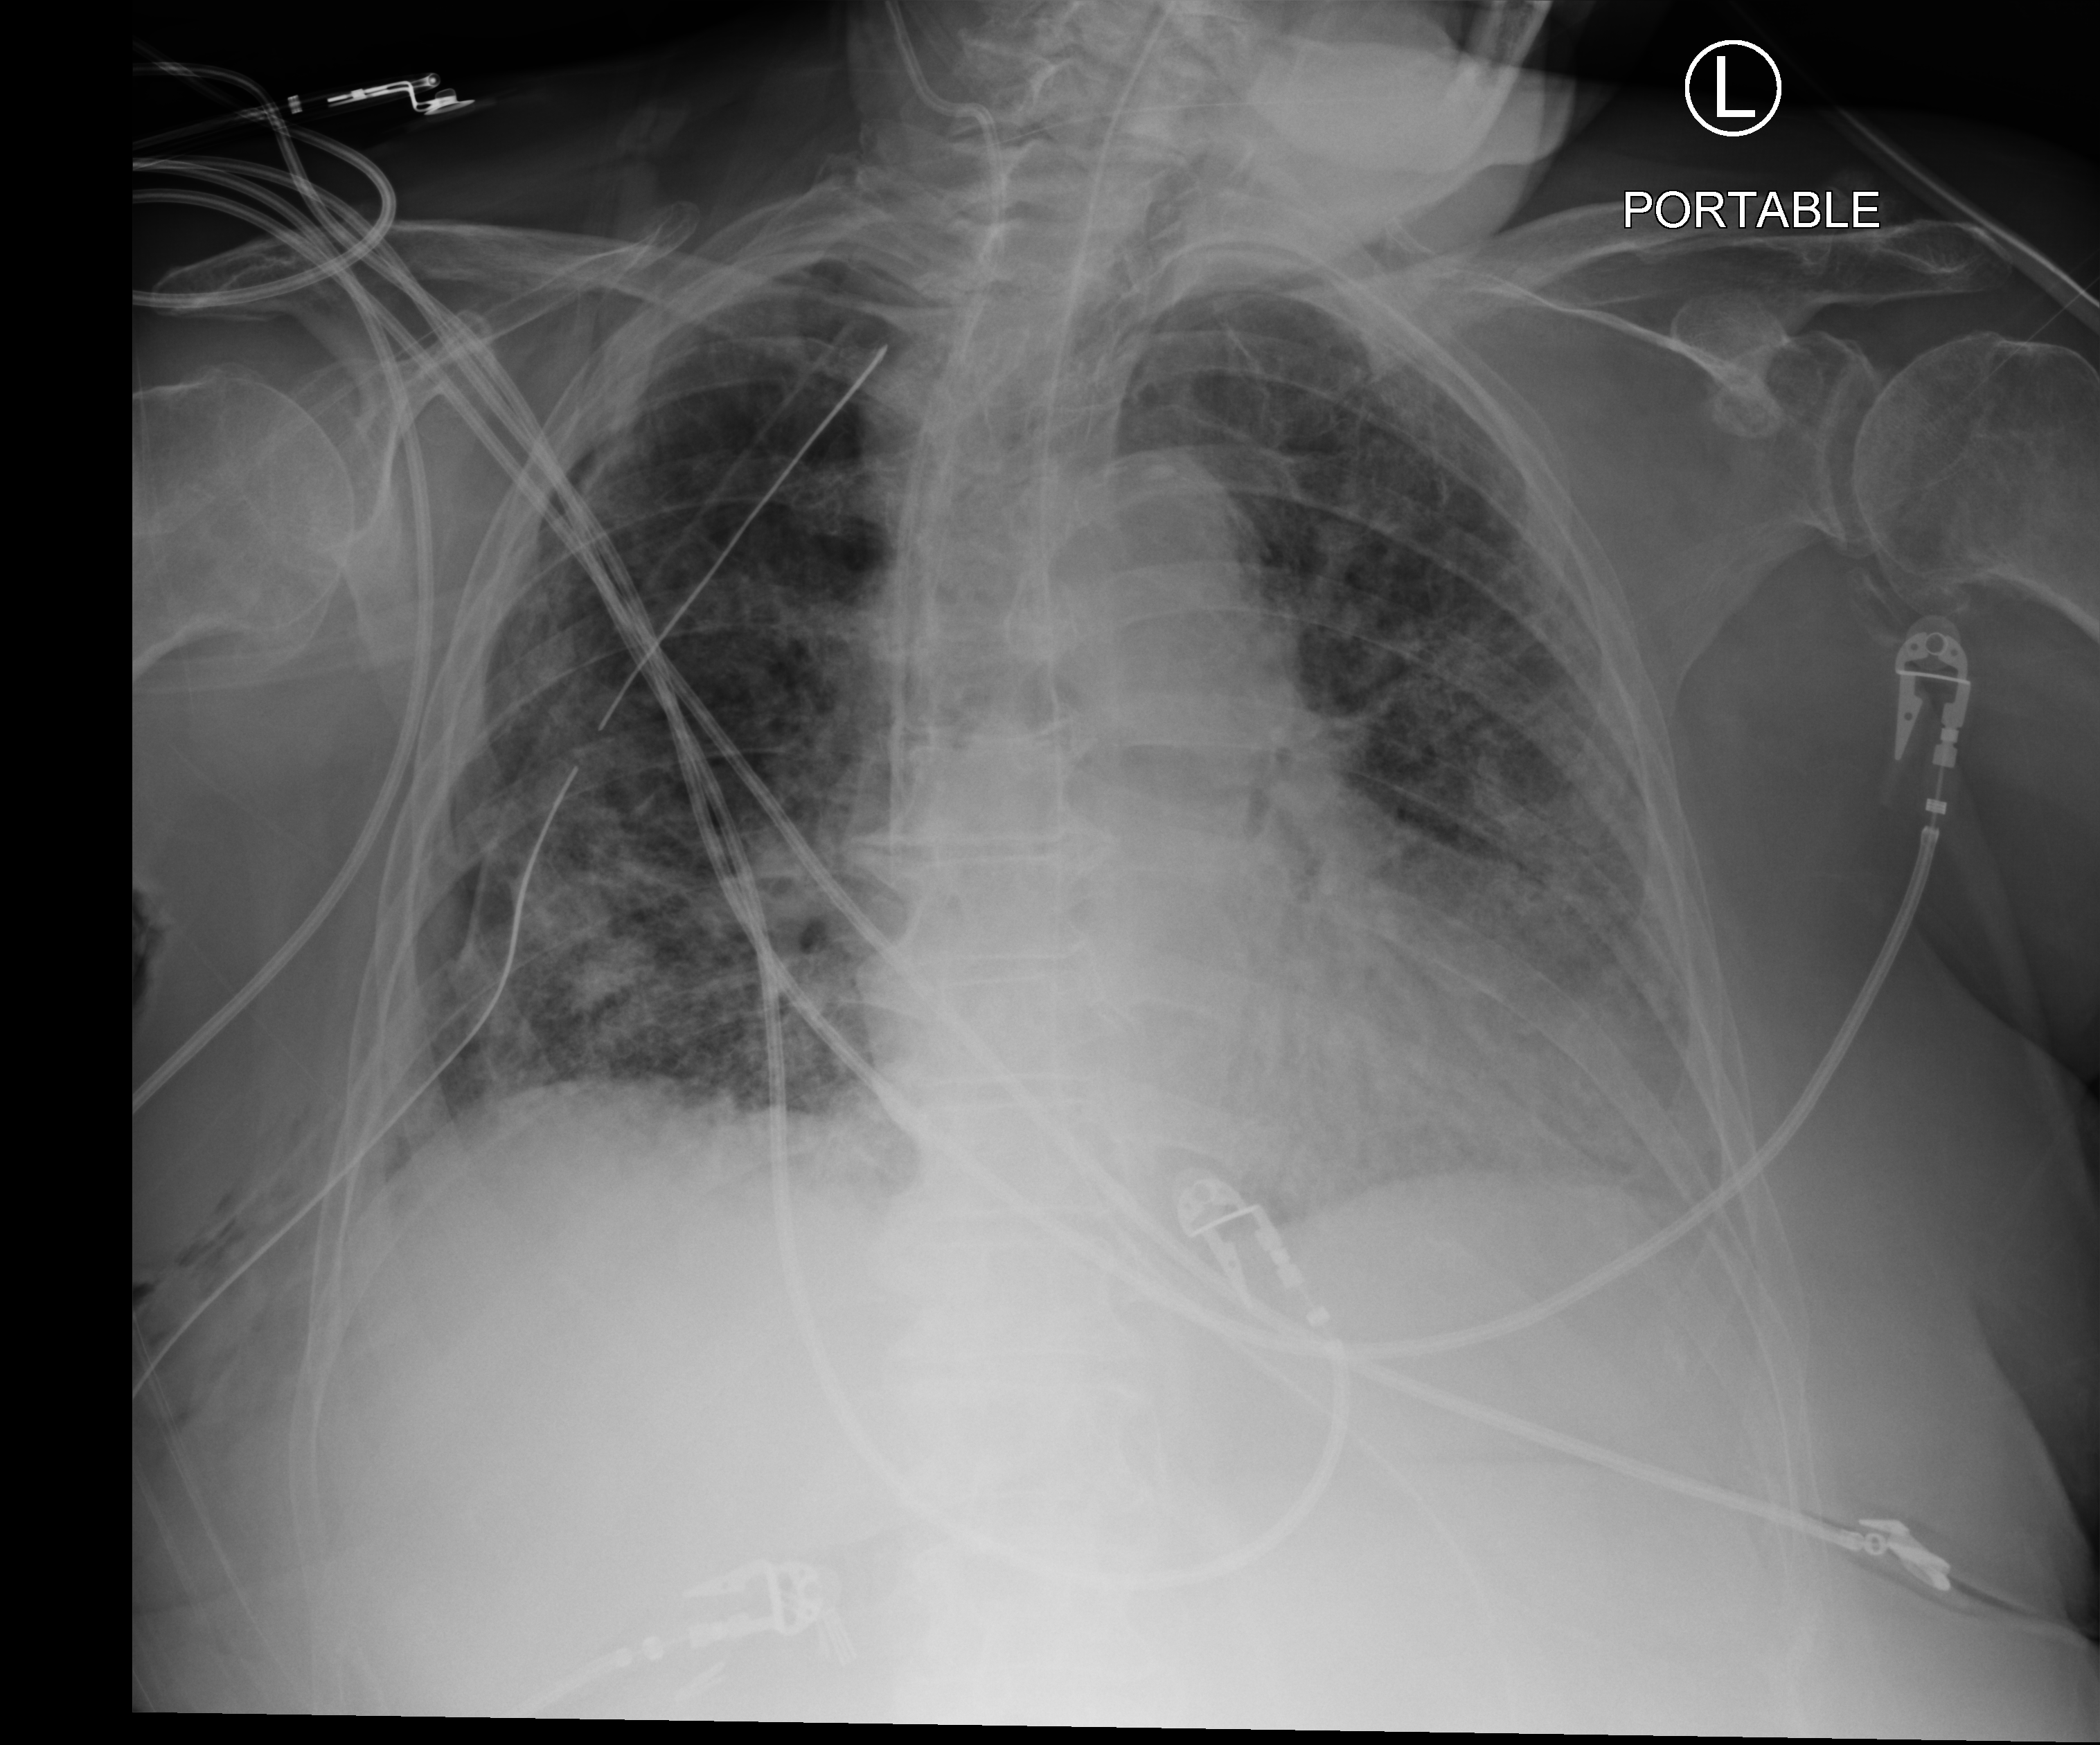
Chest X-ray (portable), anteroposterior (AP) projection. Female patient hospitalised with COVID-19, age 75–90 years.
Hospital-stay facts (about this admission, not read from this image; timing relative to this image not recorded): mechanically ventilated during this hospital stay: yes.